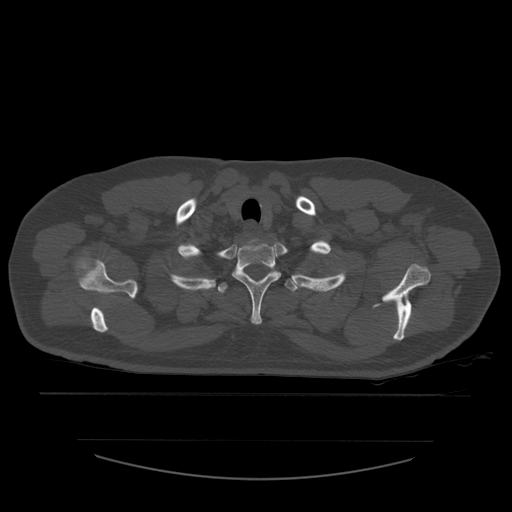
CT including the spine, one axial slice. Position 465 of 532 along the scan axis. Reconstruction kernel STANDARD. 120 kVp. Bone window (W 1800 / L 400 HU). 1.25 mm slice thickness. 512 × 512 image matrix, field of view 441 × 441 mm. Patient age 44 years. From the clinical record (not read from this slice): primary cancer: soft tissue sarcoma.
Structures marked on this image (semi-automatically segmented with operator editing):
- T1 vertebra: box from (x=233, y=242) to (x=282, y=325) px
- T2 vertebra: (x=218, y=279)–(x=313, y=294)